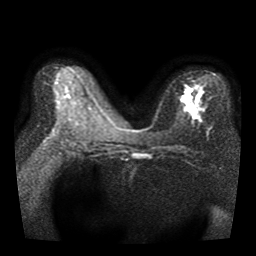
Breast MRI, one axial slice; position 18 of 40 along the scan axis; diffusion-weighted series; image 2 of 4 stored at this slice position (different b-values; order by instance number); 1.5 T; 256 × 256 image matrix, field of view 330 × 330 mm. Female patient.
Outlined on this slice (expert manual segmentation):
- tumour on diffusion-weighted imaging: bounding box <180,89,192,102> (left, top, right, bottom; pixels)